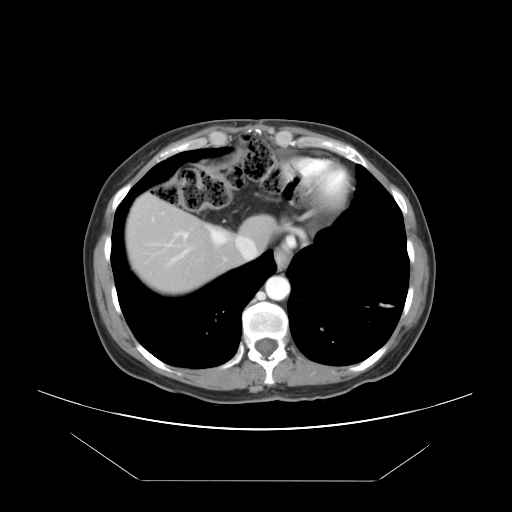
Contrast-enhanced abdominal CT, one axial slice. Position 39 of 45 along the scan axis. Reconstruction kernel STANDARD. 120 kVp. Soft-tissue window (W 400 / L 40 HU). 5 mm slice thickness. 512 × 512 image matrix, field of view 405 × 405 mm. Female patient, age 52 years. Case-level facts recorded for this patient, not image findings: diagnosis: colorectal cancer liver metastases, imaged before liver resection; multiple liver metastases: yes; largest metastasis: 2.5 cm; disease in both lobes: no.
Outlined on this slice (outlined manually by an expert reader):
- hepatic veins: bounding box (x1, y1, x2, y2) in pixels: (161, 212, 256, 267)
- liver: (127, 198, 272, 292)
- planned liver remnant (the part of the liver to remain after resection): (127, 198, 272, 281)
- portal vein (with intrahepatic branches): (175, 232, 189, 239)